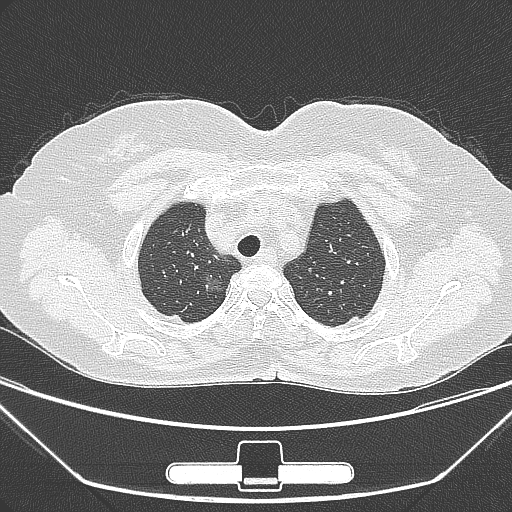
Chest CT, one axial slice. Position 234 of 275 along the scan axis. Lung window (W 1500 / L -600 HU). 1 mm slice thickness. 512 × 512 image matrix. Female patient, age 63 years. Case-level facts recorded for this patient, not image findings: clinical TNM (as recorded): T1a N0 M0.
Outlined on this slice (rectangle marked by the reading radiologist):
- lung tumour (recorded histology: adenocarcinoma): bounding box (x1, y1, x2, y2) in pixels: (195, 268, 231, 301)